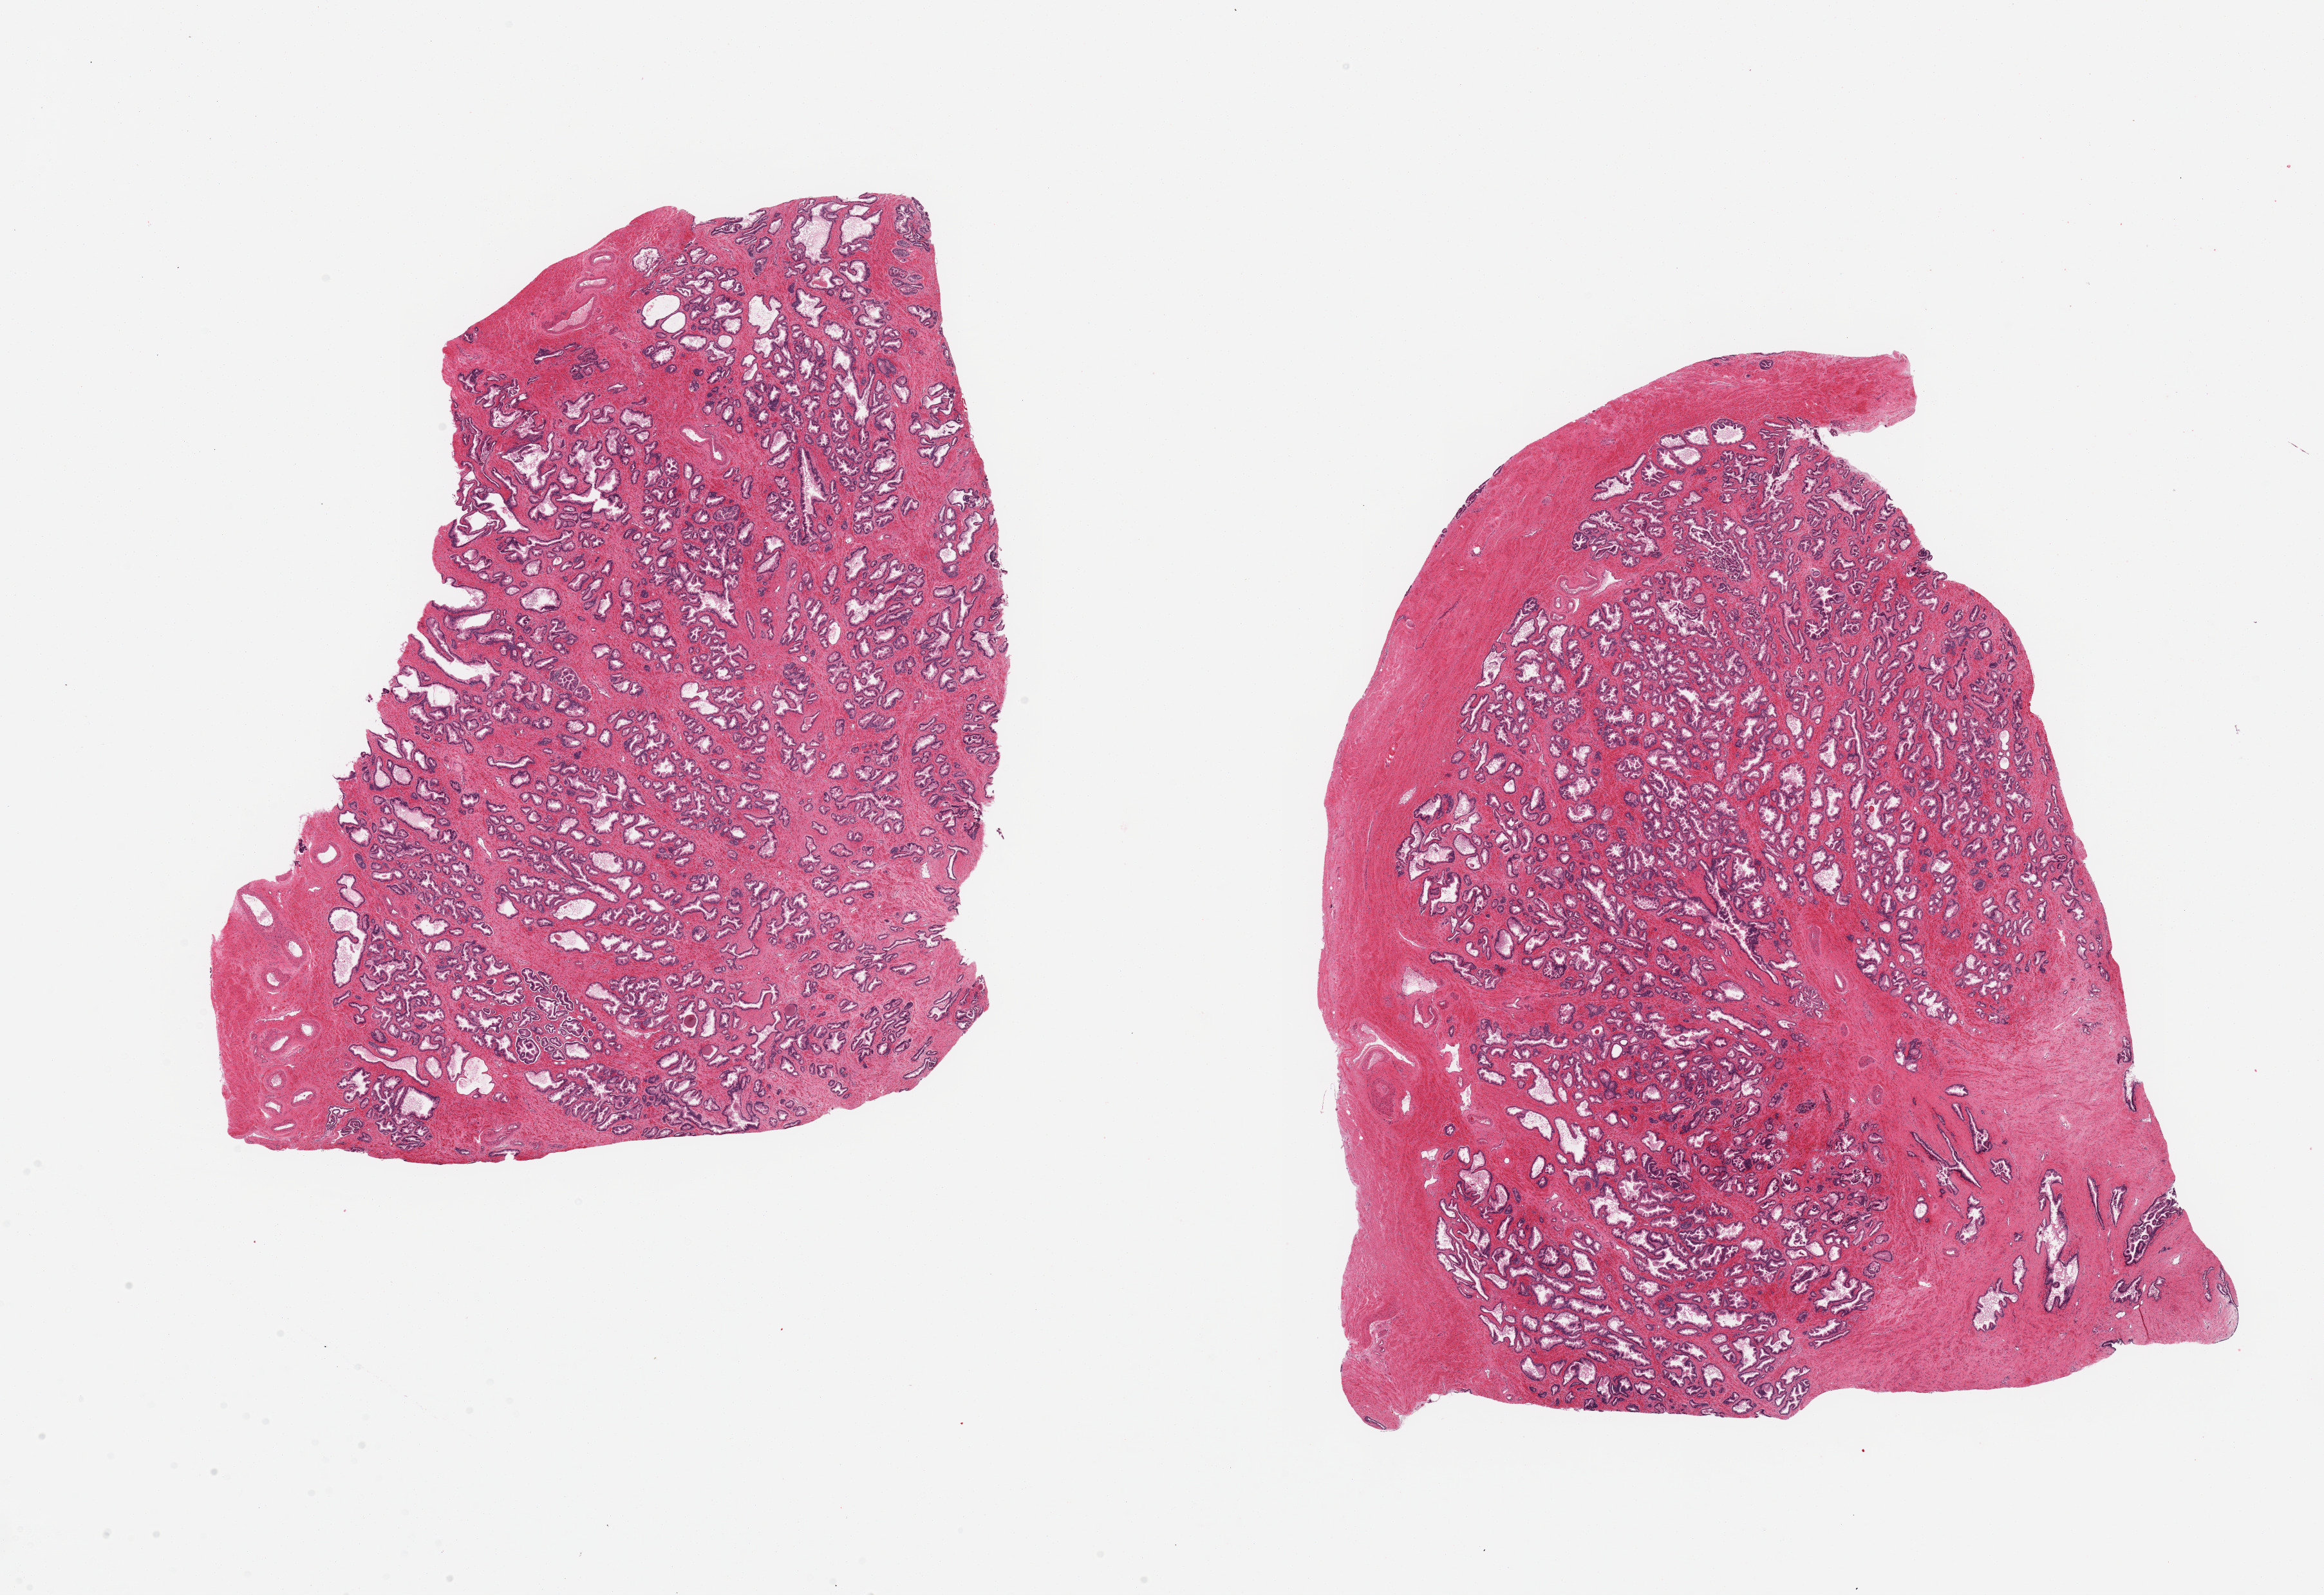
Hematoxylin and eosin (H&E) whole-slide image — shown as a low-resolution overview of the whole scanned area (about 28.5 x 19.6 mm, acquisition: 20x scan); PAXgene-fixed paraffin-embedded (PFPE) section; target tissue: prostate; tissue donor sample. Donor: male.
Review note (as recorded): 2 pieces, prominent glandular hyperplastic pattern.